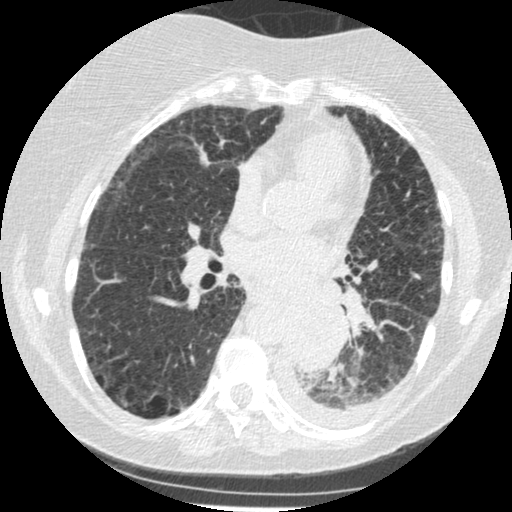
Low-dose screening chest CT, one axial slice; position 119 of 341 along the scan axis; reconstruction kernel STANDARD; 120 kVp; lung window (W 1500 / L -600 HU); 1.25 mm slice thickness; 512 × 512 image matrix.
Structures marked on this image (outlined manually by an expert reader):
- lesion 1 (tumor, lower lobe of left lung): bounding box <283,301,344,370> (left, top, right, bottom; pixels)